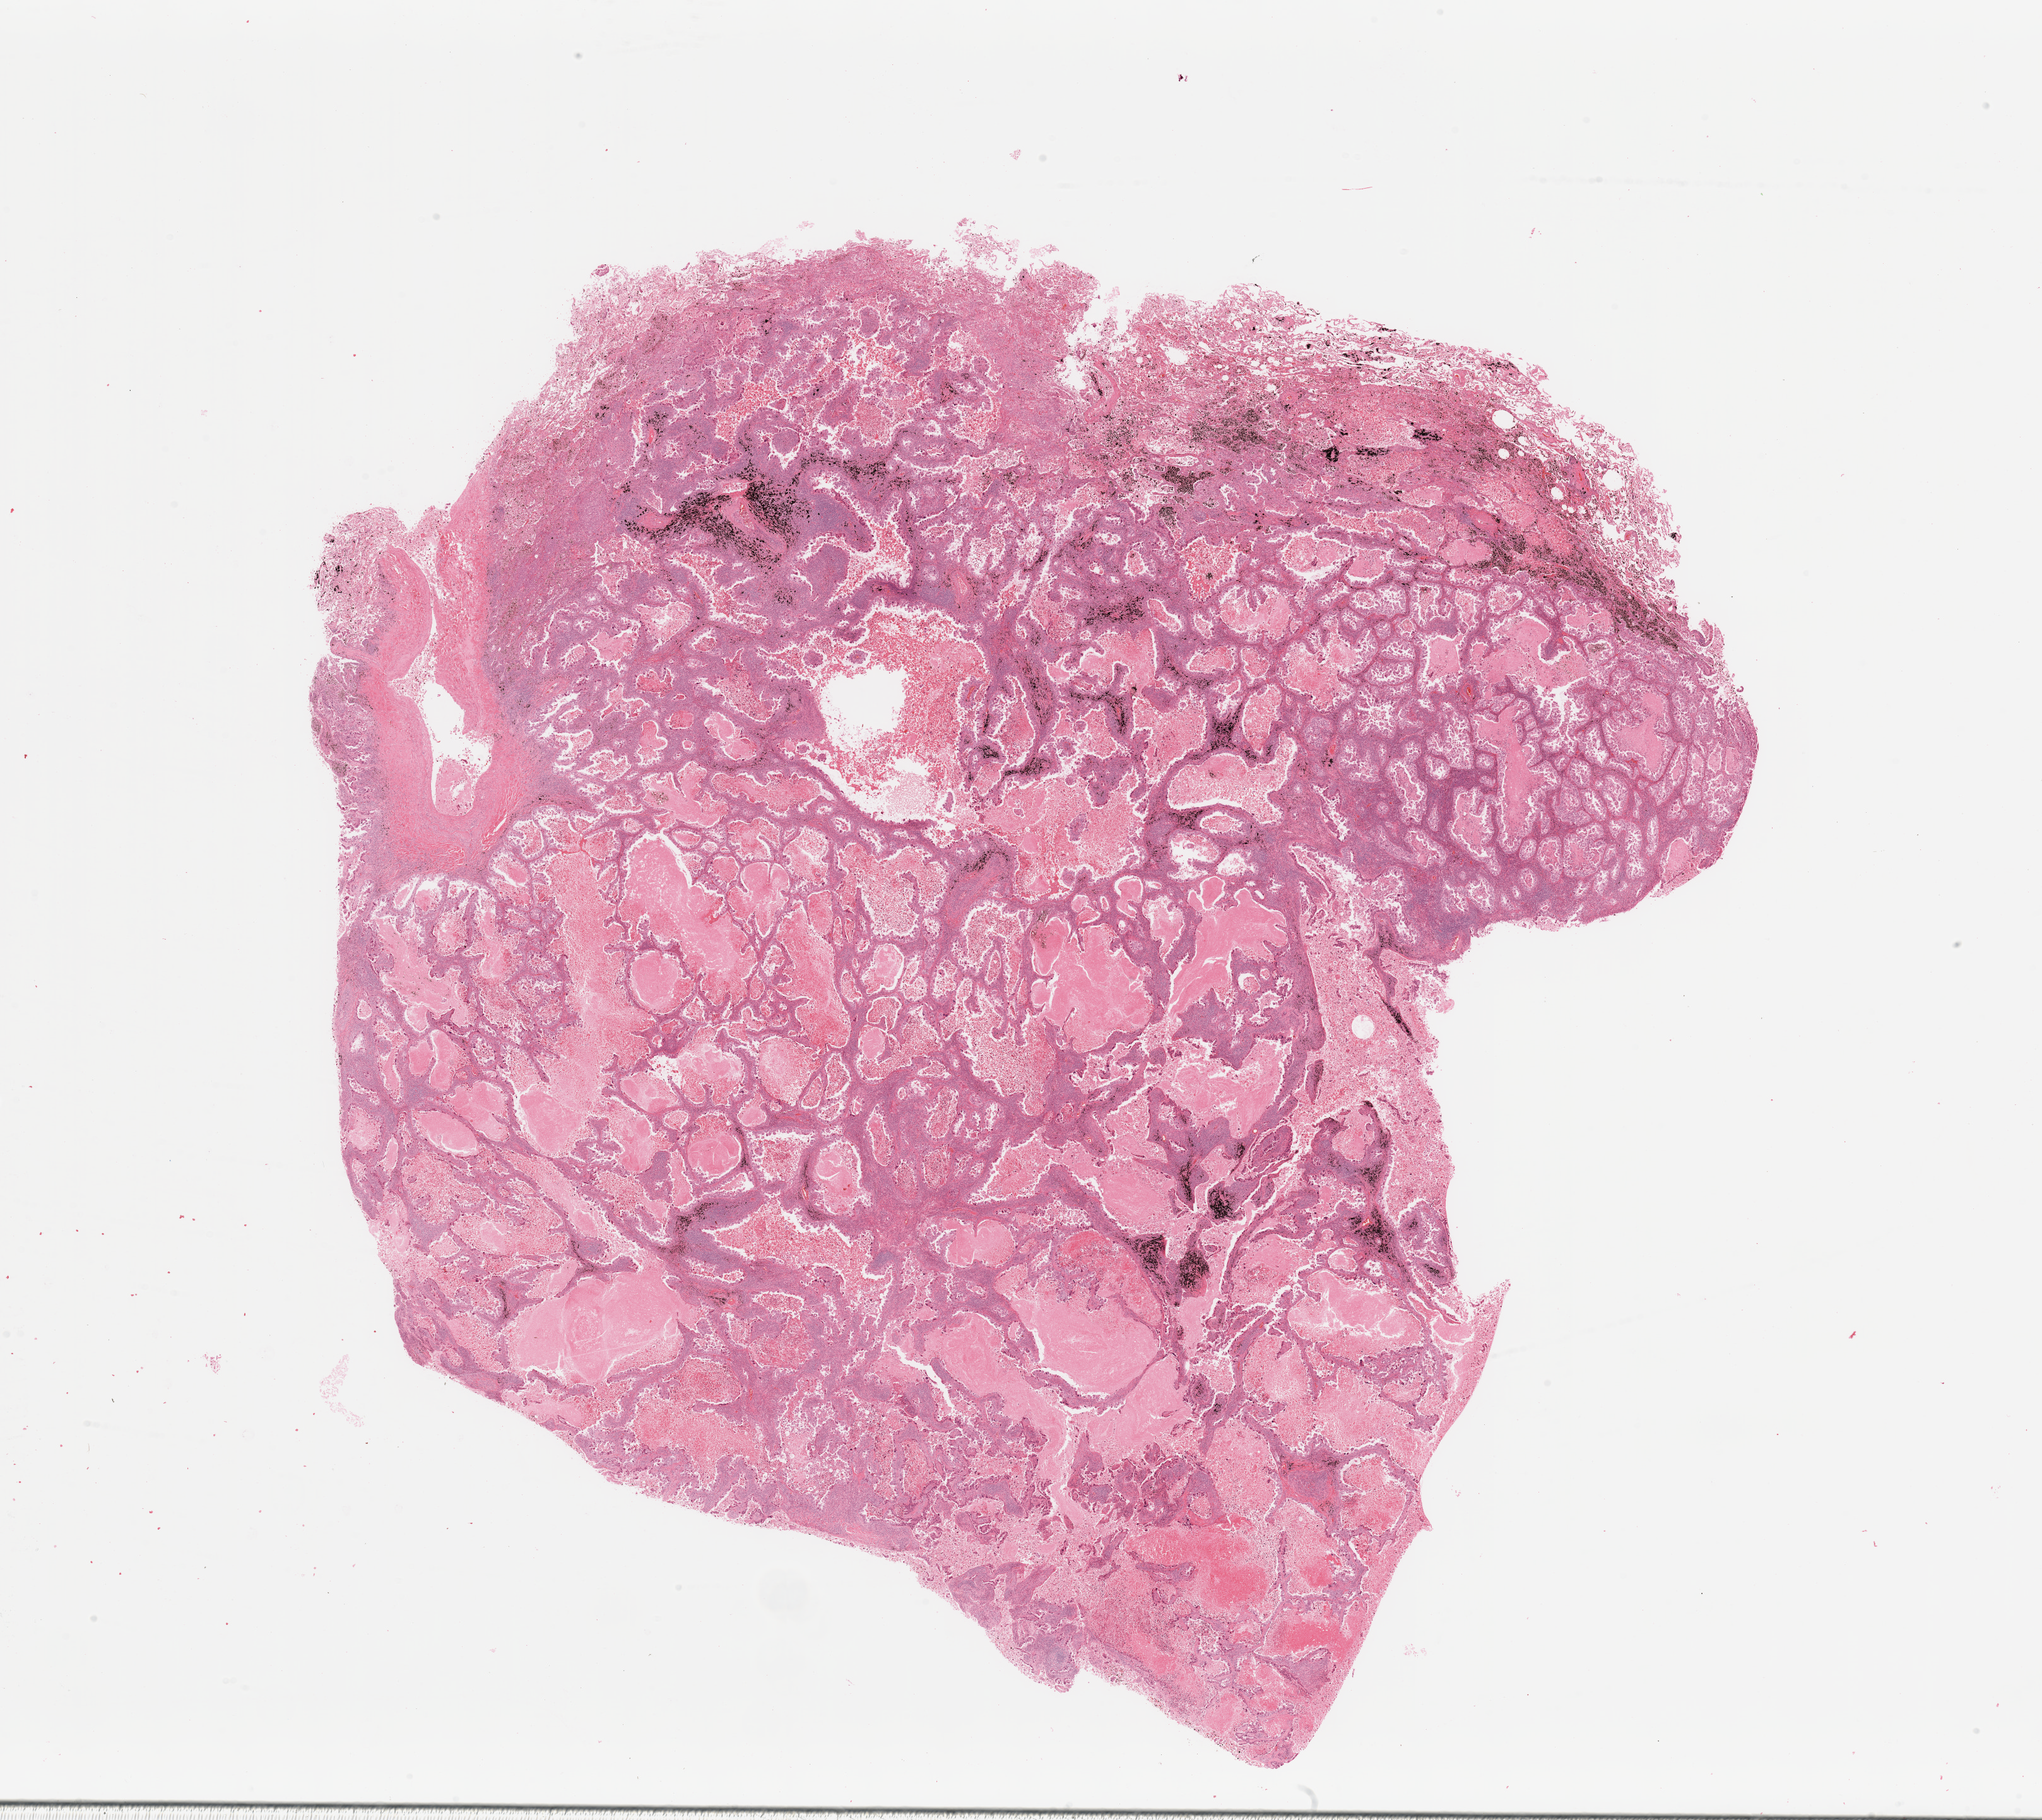
Whole-slide histology image, H&E — shown as a low-resolution overview of the whole scanned area (about 25.6 x 22.8 mm, slide scanned at 20x). Tumour tissue sample, lung. 57-year-old male patient. Histologic grade: G2 (moderately differentiated).
AJCC pathologic stage: IIIA. Diagnosis: Adenocarcinoma, NOS.